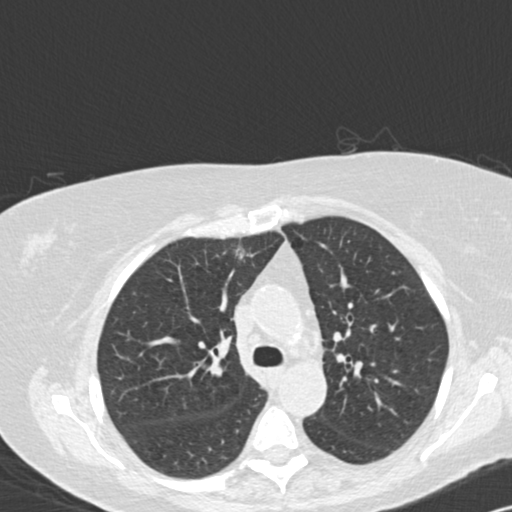
Low-dose screening chest CT, one axial slice. Slice 99 of 141 in the series (ordered by position). Reconstruction kernel B30f. 120 kVp. Lung window (W 1500 / L -600 HU). 2 mm slice thickness. 512 × 512 image matrix, field of view 328 × 328 mm.
Structures marked on this image (manually delineated by an expert):
- lesion 1 (tumor, upper lobe of right lung): bounding box [x1, y1, x2, y2] px = [239, 252, 245, 259]